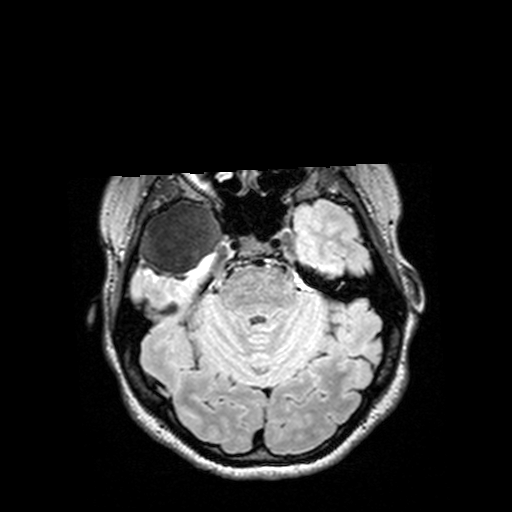
Brain MRI from a brain-tumour surgery series, one axial slice. Slice 101 of 144 in the series (ordered by position). T2 FLAIR. 1 mm slice thickness. 512 × 512 image matrix, field of view 250 × 250 mm. From the clinical record (not read from this slice): histopathology: Astrocytoma; WHO grade: 3; IDH mutation: yes; tumour location: Right Insular Temporal.
Structures marked on this image (outlined manually by an expert reader):
- tumour: bounding box [x1, y1, x2, y2] px = [126, 199, 232, 280]